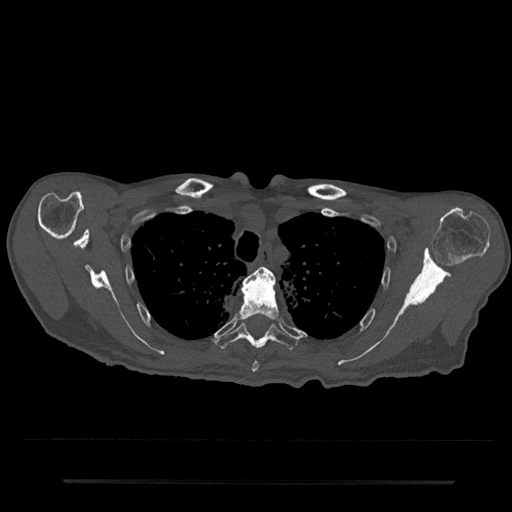
CT including the spine, one axial slice. Bone window (W 1800 / L 400 HU). 0.5 mm slice thickness. 512 × 512 image matrix. Patient: male, 74 years. From the clinical record (not read from this slice): primary cancer: prostate.
Outlined on this slice (semi-automatically segmented with operator editing):
- T3 vertebra: box from (x=246, y=267) to (x=274, y=280) px
- T4 vertebra: (x=238, y=272)–(x=279, y=373)
- T5 vertebra: (x=214, y=320)–(x=299, y=351)